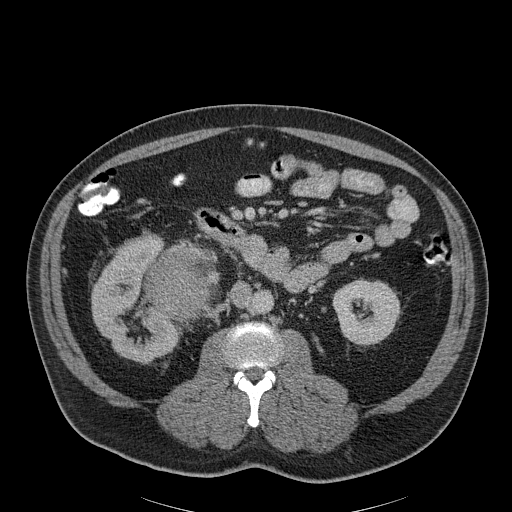
Contrast-enhanced abdominal CT, one axial slice; slice 105 of 186 in the series (ordered by position); reconstruction kernel B30f; soft-tissue window (W 400 / L 40 HU); 512 × 512 image matrix, field of view 464 × 464 mm. Patient: male, 56 years. From the clinical record (not read from this slice): diagnosis: adrenocortical carcinoma; tumour side: right adrenal; tumour size at pathology: 18 cm; Ki-67 index: 2 %; stage (as recorded): 3.
Annotated regions visible in this slice (semi-automatically segmented with operator editing):
- mass: bounding box [x1, y1, x2, y2] px = [145, 250, 212, 318]